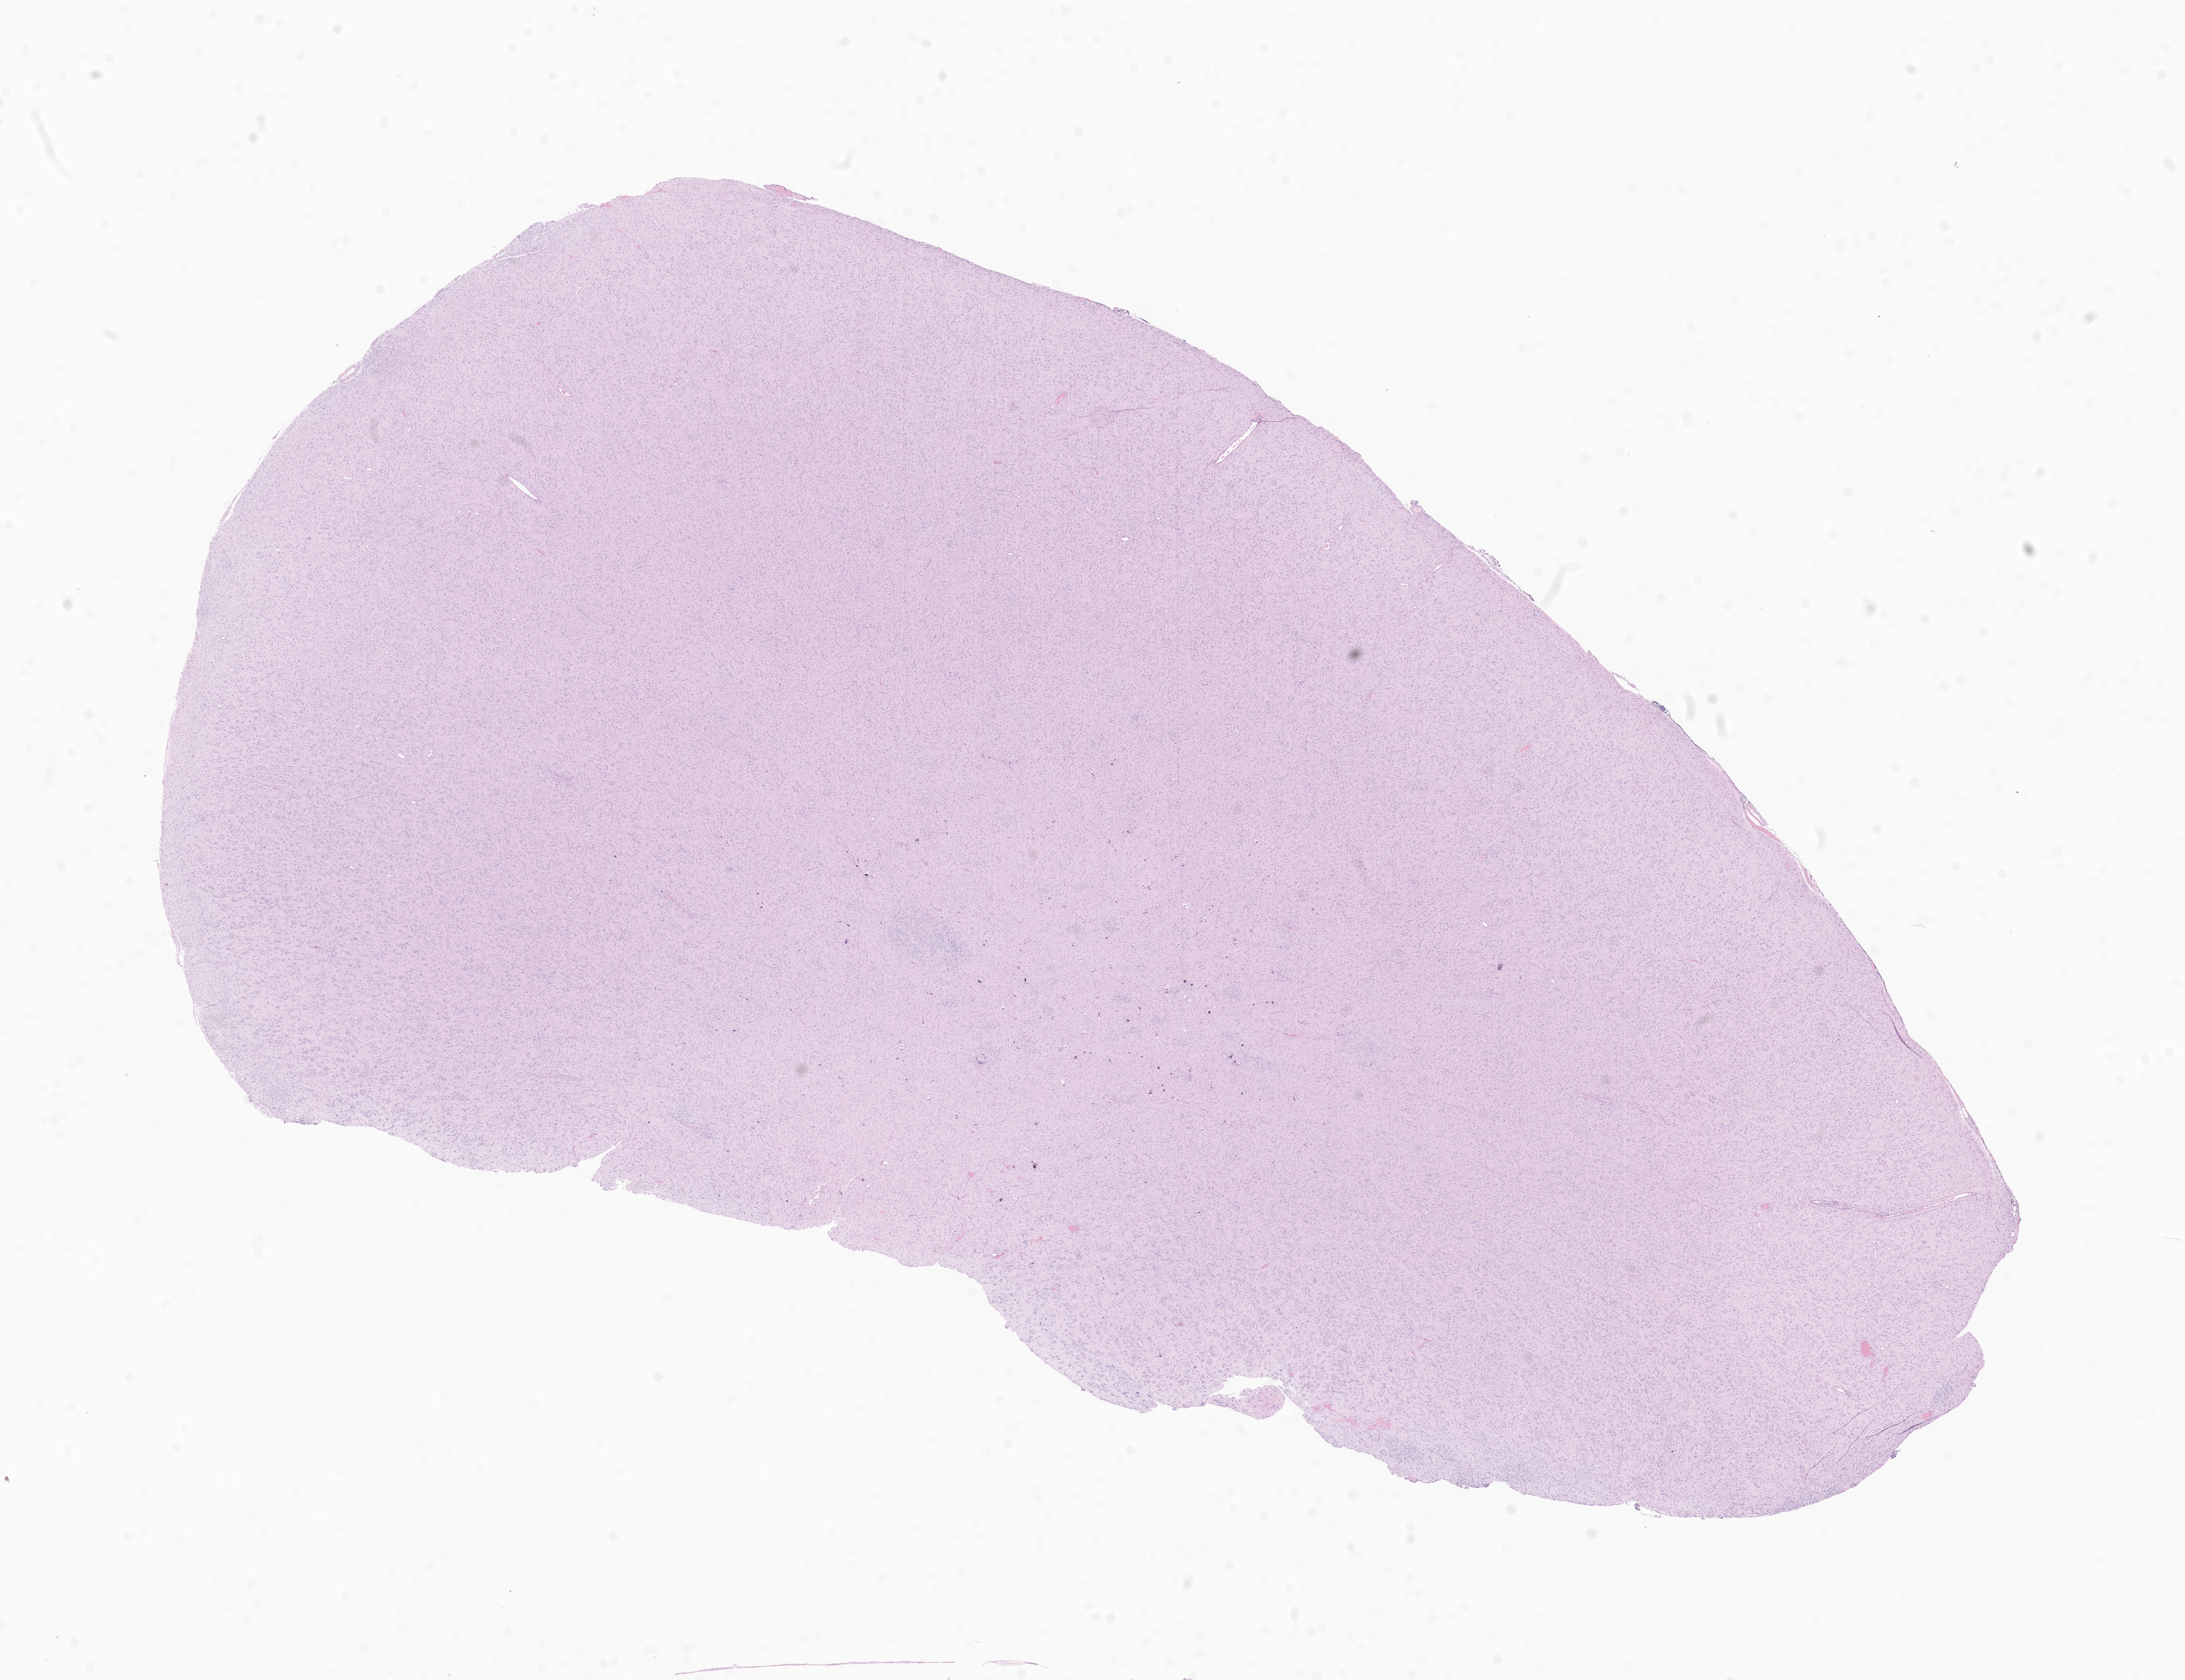
Digitized haematoxylin and eosin-stained section of tumor tissue from the temporal lobe — low-resolution overview of the scanned area, about 25.0 x 19.2 mm; FFPE section. Female patient, age 581 days (about 1.6 years).
Diagnosis: Neoplasm, malignant.